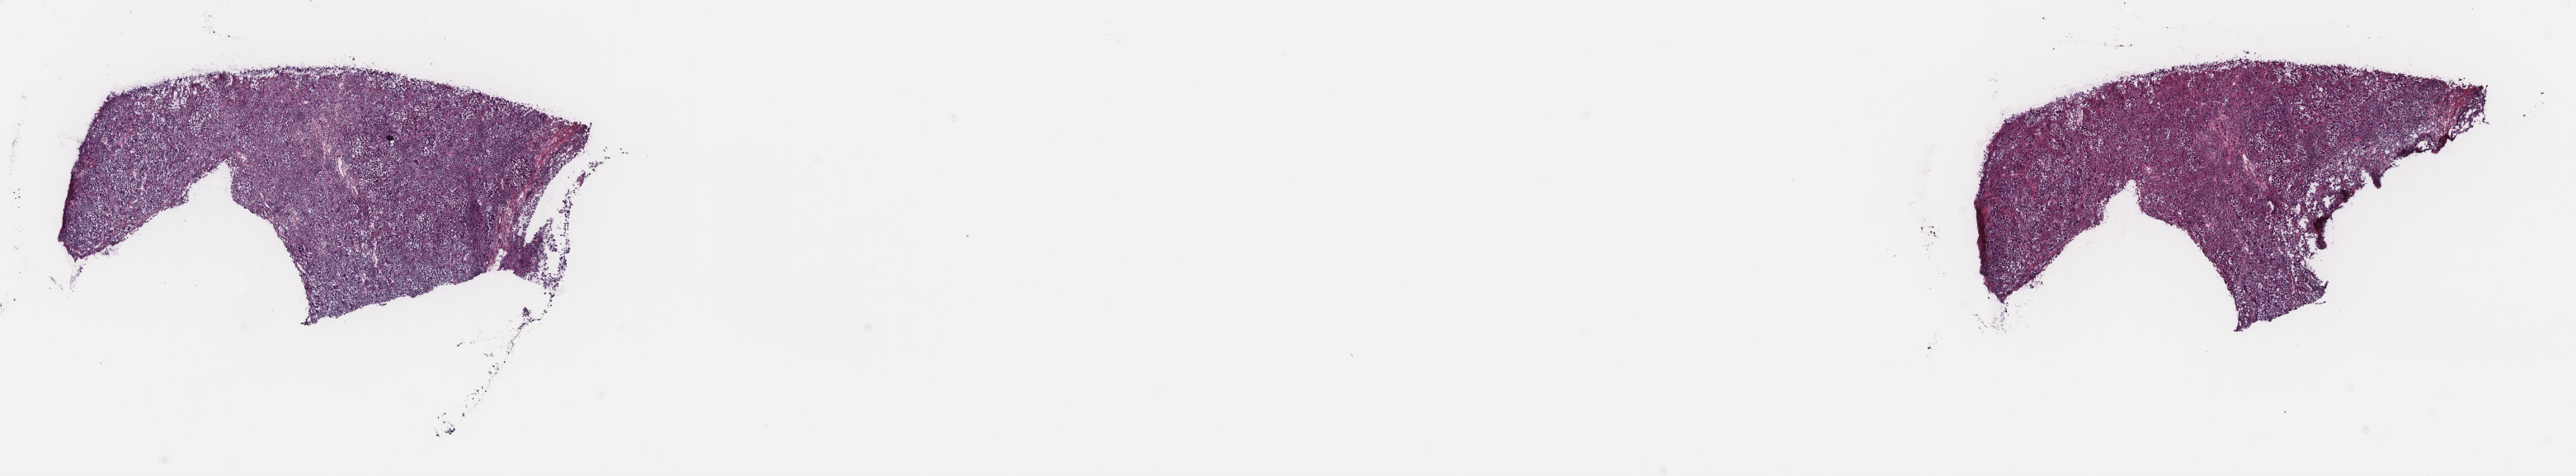
H&E-stained whole-slide image — a low-resolution overview of the entire scanned area, about 24.8 x 4.6 mm. Frozen section from the top of the tissue portion. Metastatic tumour sample, sampled site: lymph nodes of axilla or arm. Female, age 29 years at initial diagnosis. Pathologist review of this section (percent, as recorded): tumour cells 60%, tumour nuclei 60%, normal cells 0%, stromal cells 40%, necrosis 0%. Inflammatory infiltration, as recorded: lymphocyte infiltration 25%, monocyte infiltration 2%, neutrophil infiltration 2%.
This section: metastatic tumour tissue. Patient diagnosis: Malignant melanoma, NOS.